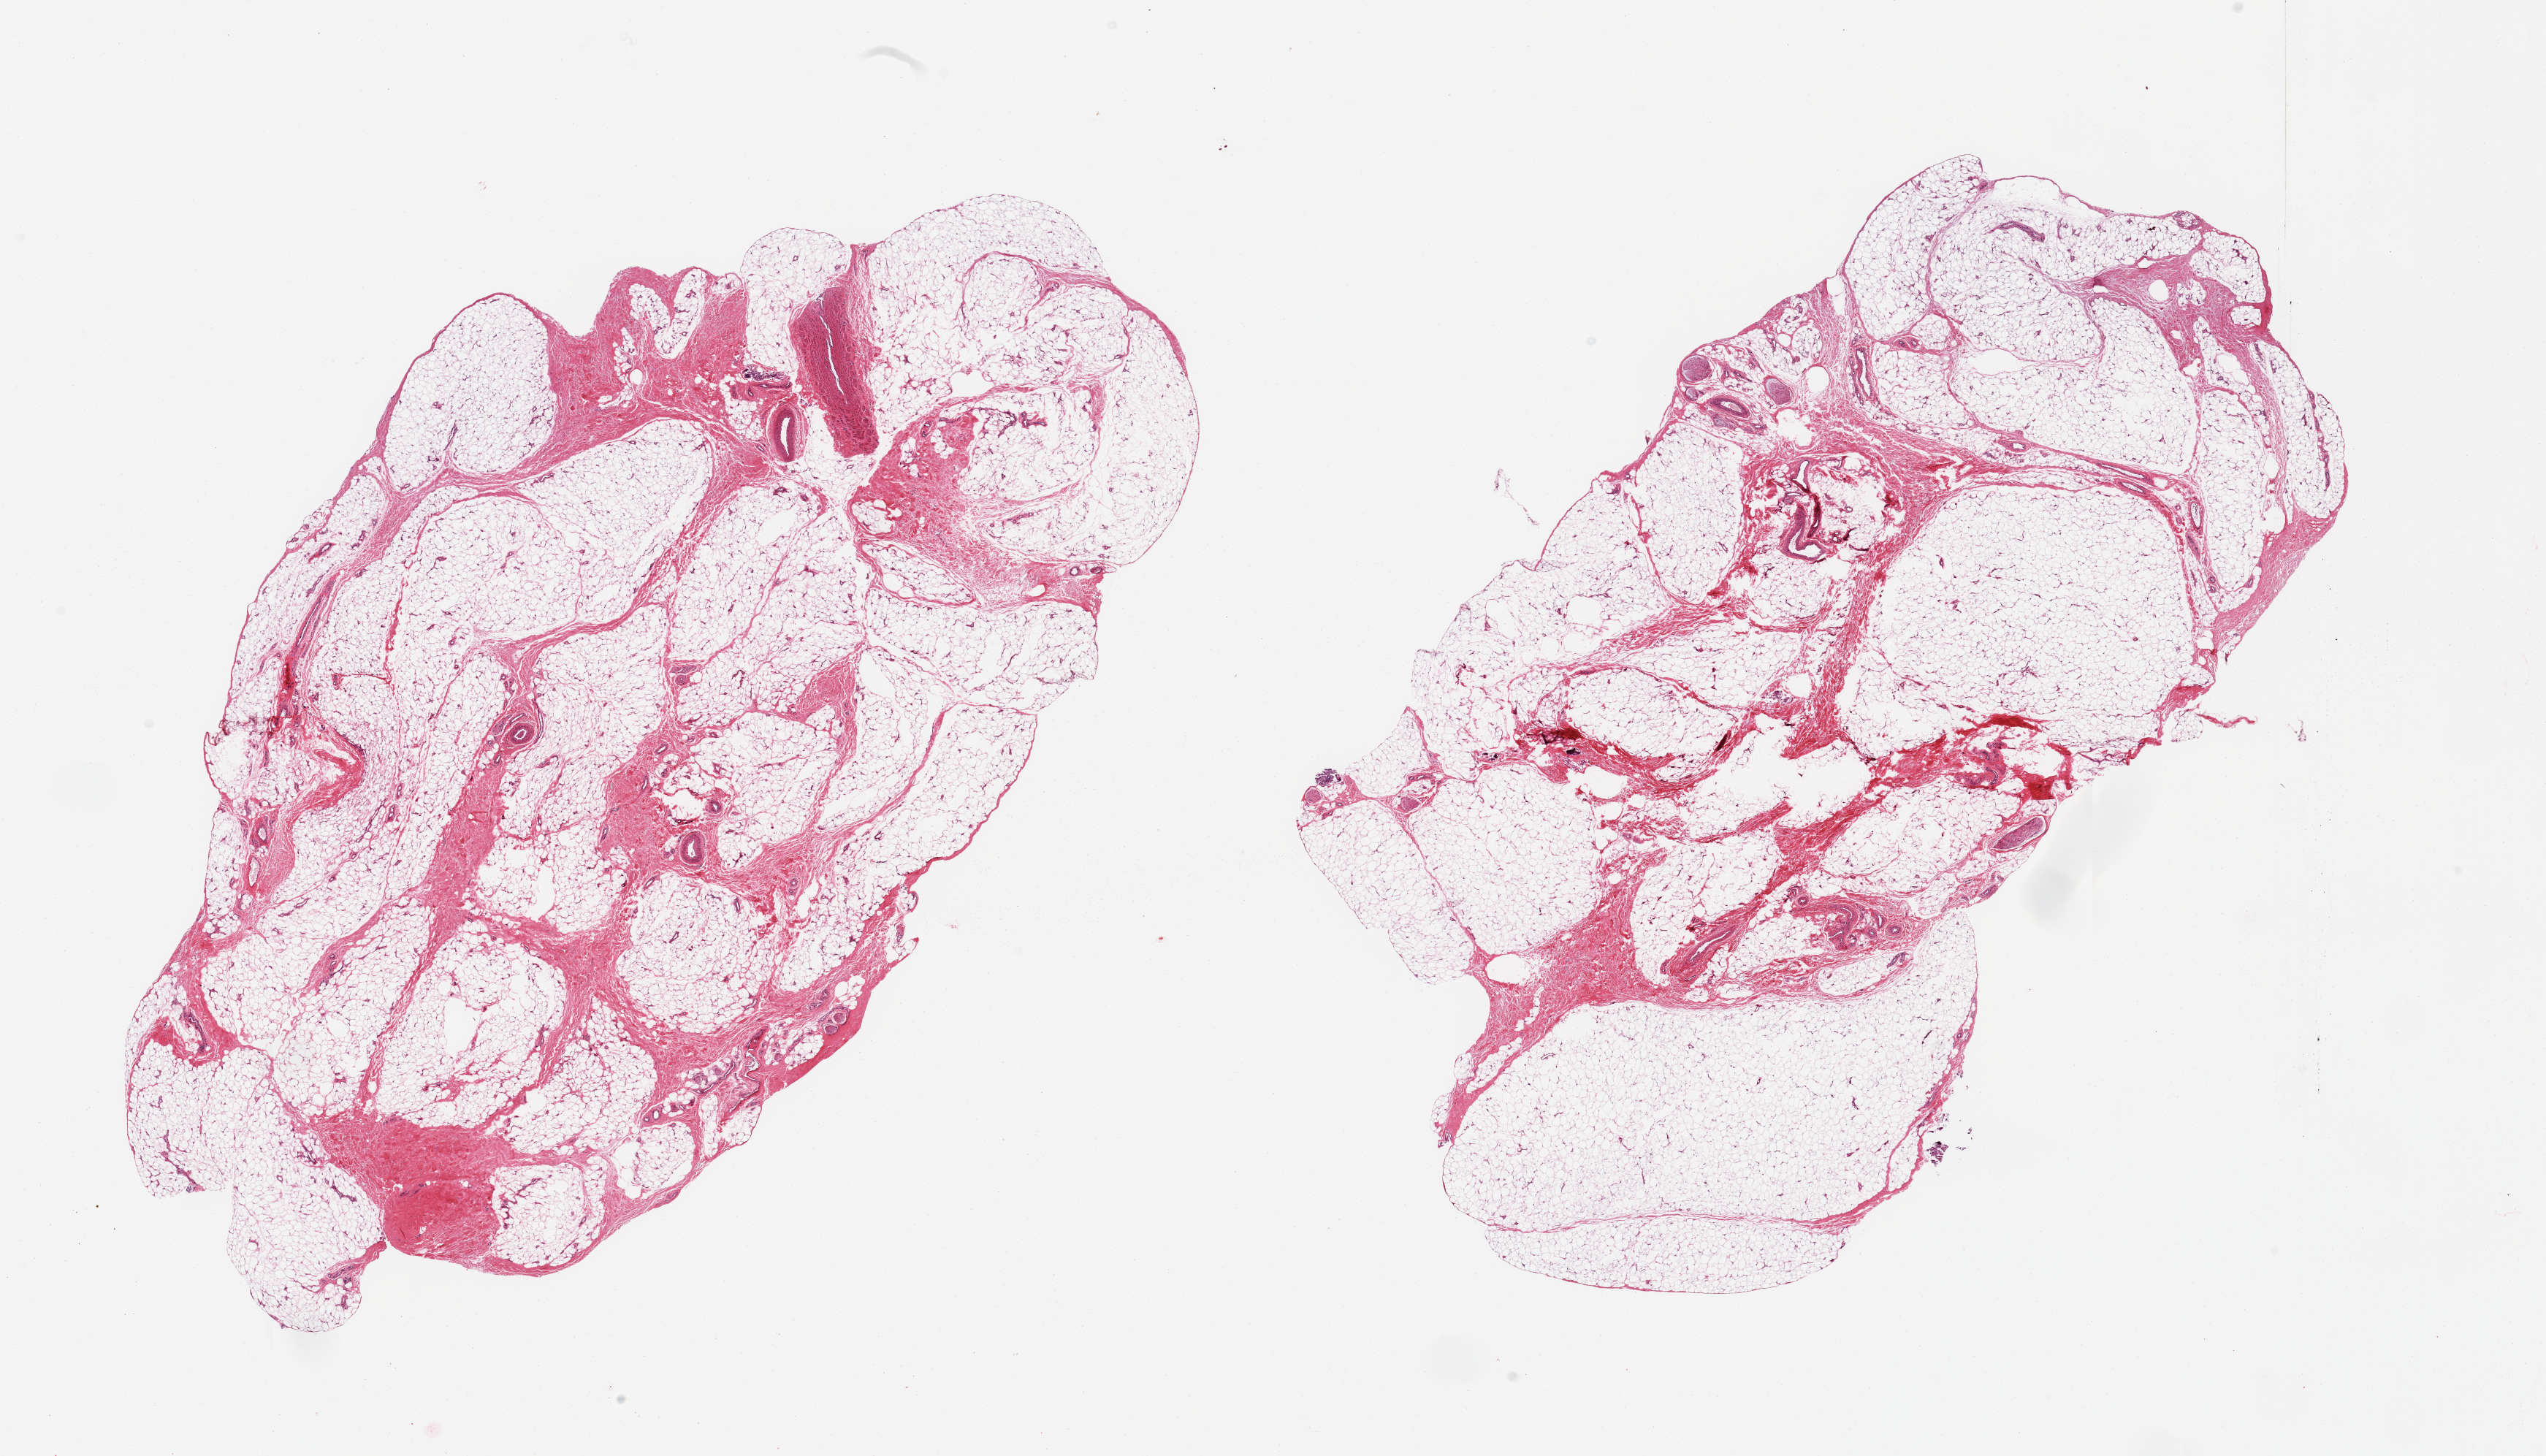
Digitized haematoxylin and eosin-stained section, low-resolution overview of the scanned area, about 27.6 x 15.8 mm (acquisition: 20x scan); PAXgene-fixed, paraffin-embedded tissue; section of adipose tissue (target tissue); donor tissue sample. Male donor.
Review note (as recorded): 2 pieces; fat with 10-15% fibrous tissue/vessels/nerve.